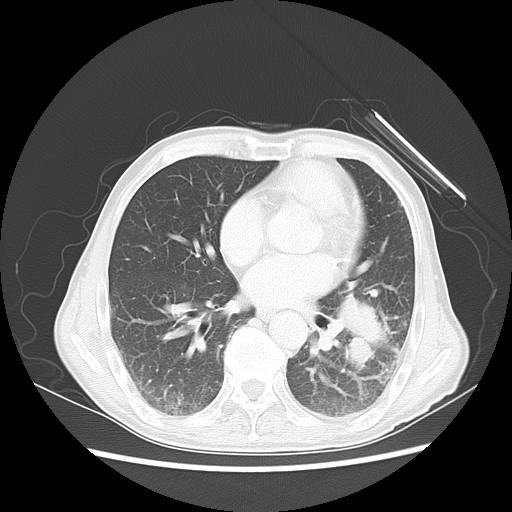
Chest CT, one axial slice. Slice 23 of 51 in the series (ordered by position). Lung window (W 1500 / L -600 HU). 5 mm slice thickness. 512 × 512 image matrix. Patient: male, 64 years. From the clinical record (not read from this slice): clinical TNM (as recorded): T4 N0 M0; histopathological grade: G2-3.
Annotated regions visible in this slice (bounding box drawn by a radiologist):
- lung tumour (recorded histology: squamous cell carcinoma): box from (x=325, y=283) to (x=397, y=374) px